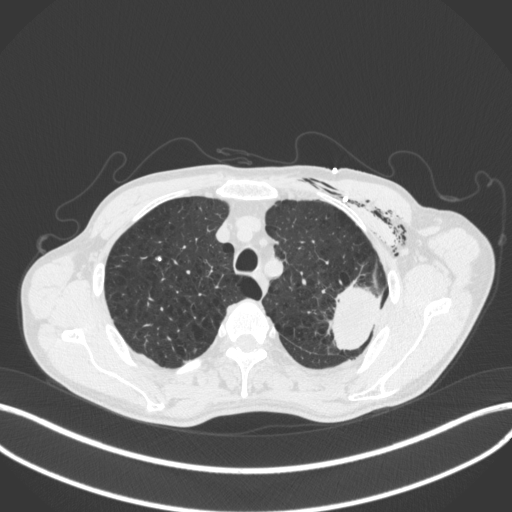
Chest CT, one axial slice; position 328 of 416 along the scan axis; reconstruction kernel B31f; 120 kVp; lung window (W 1500 / L -600 HU); 1 mm slice thickness; 512 × 512 image matrix, field of view 400 × 400 mm. Patient: male, 58 years. Case-level facts recorded for this patient, not image findings: clinical TNM (as recorded): T3 N0 M0.
Annotated regions visible in this slice (bounding box drawn by a radiologist):
- lung tumour (recorded histology: adenocarcinoma): bounding box (x1, y1, x2, y2) in pixels: (319, 282, 389, 355)